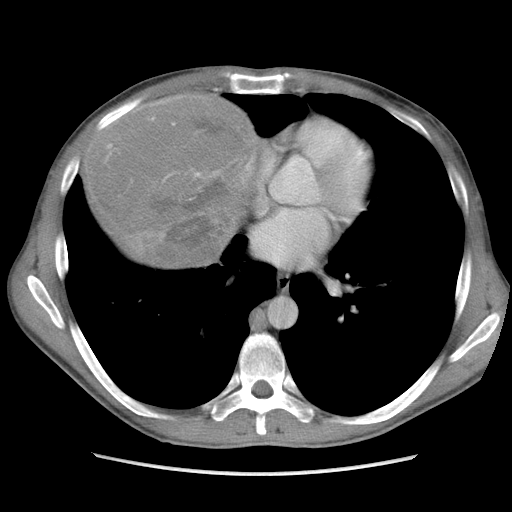
Contrast-enhanced abdominal CT, one axial slice. Slice 100 of 115 in the series (ordered by position). Soft-tissue window (W 400 / L 40 HU). 512 × 512 image matrix. Male patient. From the clinical record (not read from this slice): diagnosis: adrenocortical carcinoma; tumour side: right adrenal; Ki-67 index: 13 %; stage (as recorded): 3.
Outlined on this slice (semi-automatic segmentation, software-assisted and operator-edited):
- mass: box from (x=81, y=93) to (x=260, y=266) px